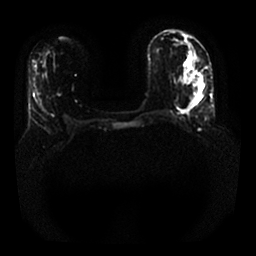
Breast MRI, one axial slice. Slice 7 of 25 in the series (ordered by position). Diffusion-weighted series; image 2 of 4 stored at this slice position (different b-values; order by instance number). 1.5 T. 256 × 256 image matrix. Female patient.
Annotated regions visible in this slice (manually delineated by an expert):
- tumour on diffusion-weighted imaging: bounding box [x1, y1, x2, y2] px = [193, 84, 203, 102]